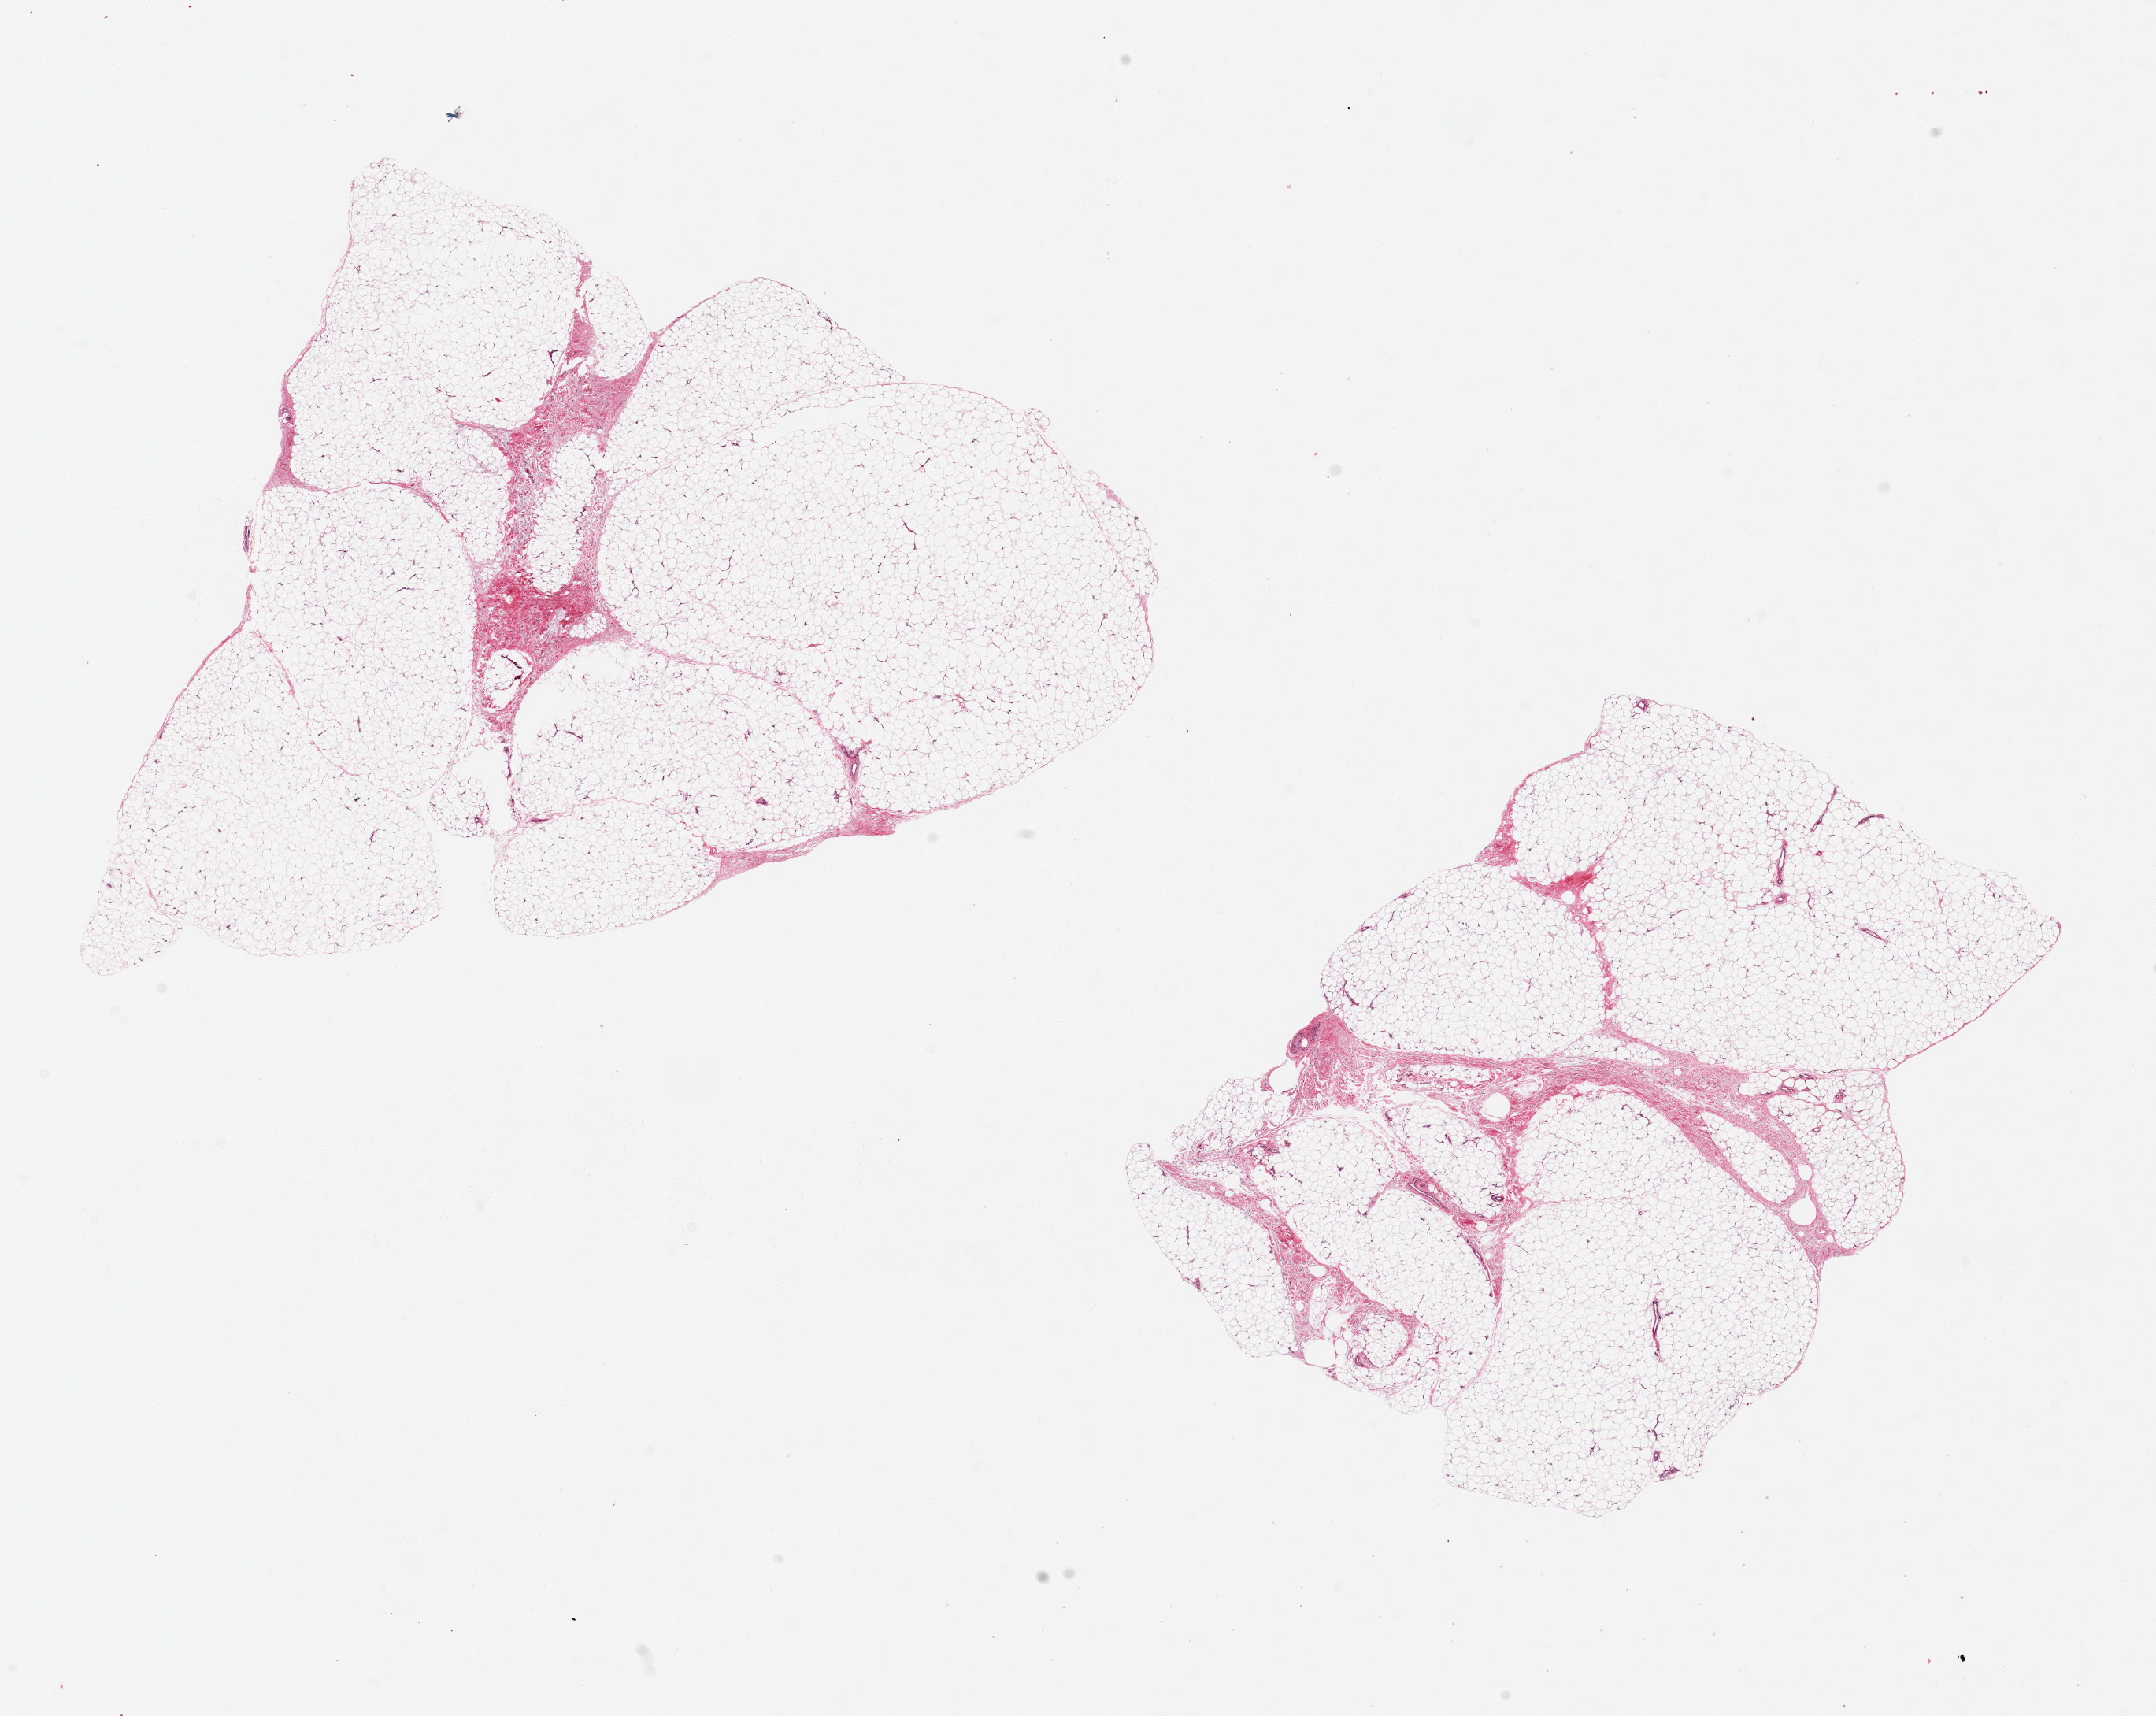
Whole-slide image, H&E stain — whole scanned area (about 21.7 x 17.2 mm, slide scanned at 20x) shown as a low-resolution overview. PAXgene-fixed paraffin-embedded (PFPE) section. Target tissue: adipose tissue. Tissue donor sample. Donor sex: male.
Pathologist's review note for this sample: 2 pieces, 11x9 & 8x6mm.